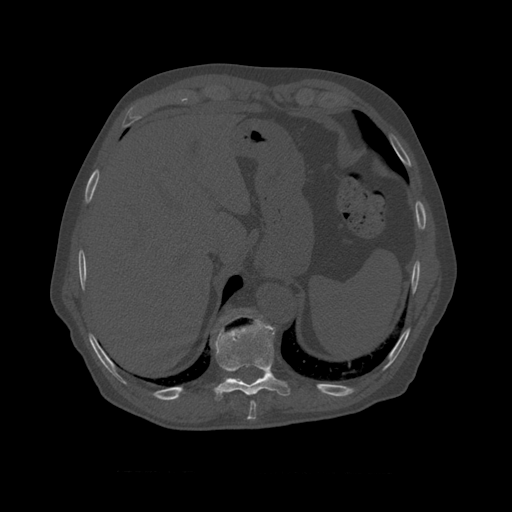
CT including the spine, one axial slice. Slice 422 of 450 in the series (ordered by position). Reconstruction kernel STANDARD. 120 kVp. Bone window (W 1800 / L 400 HU). 512 × 512 image matrix. Patient age 75 years. From the clinical record (not read from this slice): primary cancer: prostate.
Annotated regions visible in this slice (semi-automatically segmented with operator editing):
- T10 vertebra: bounding box (x1, y1, x2, y2) in pixels: (225, 309, 253, 325)
- T8 vertebra: (250, 401, 257, 411)
- T9 vertebra: (214, 317, 291, 397)